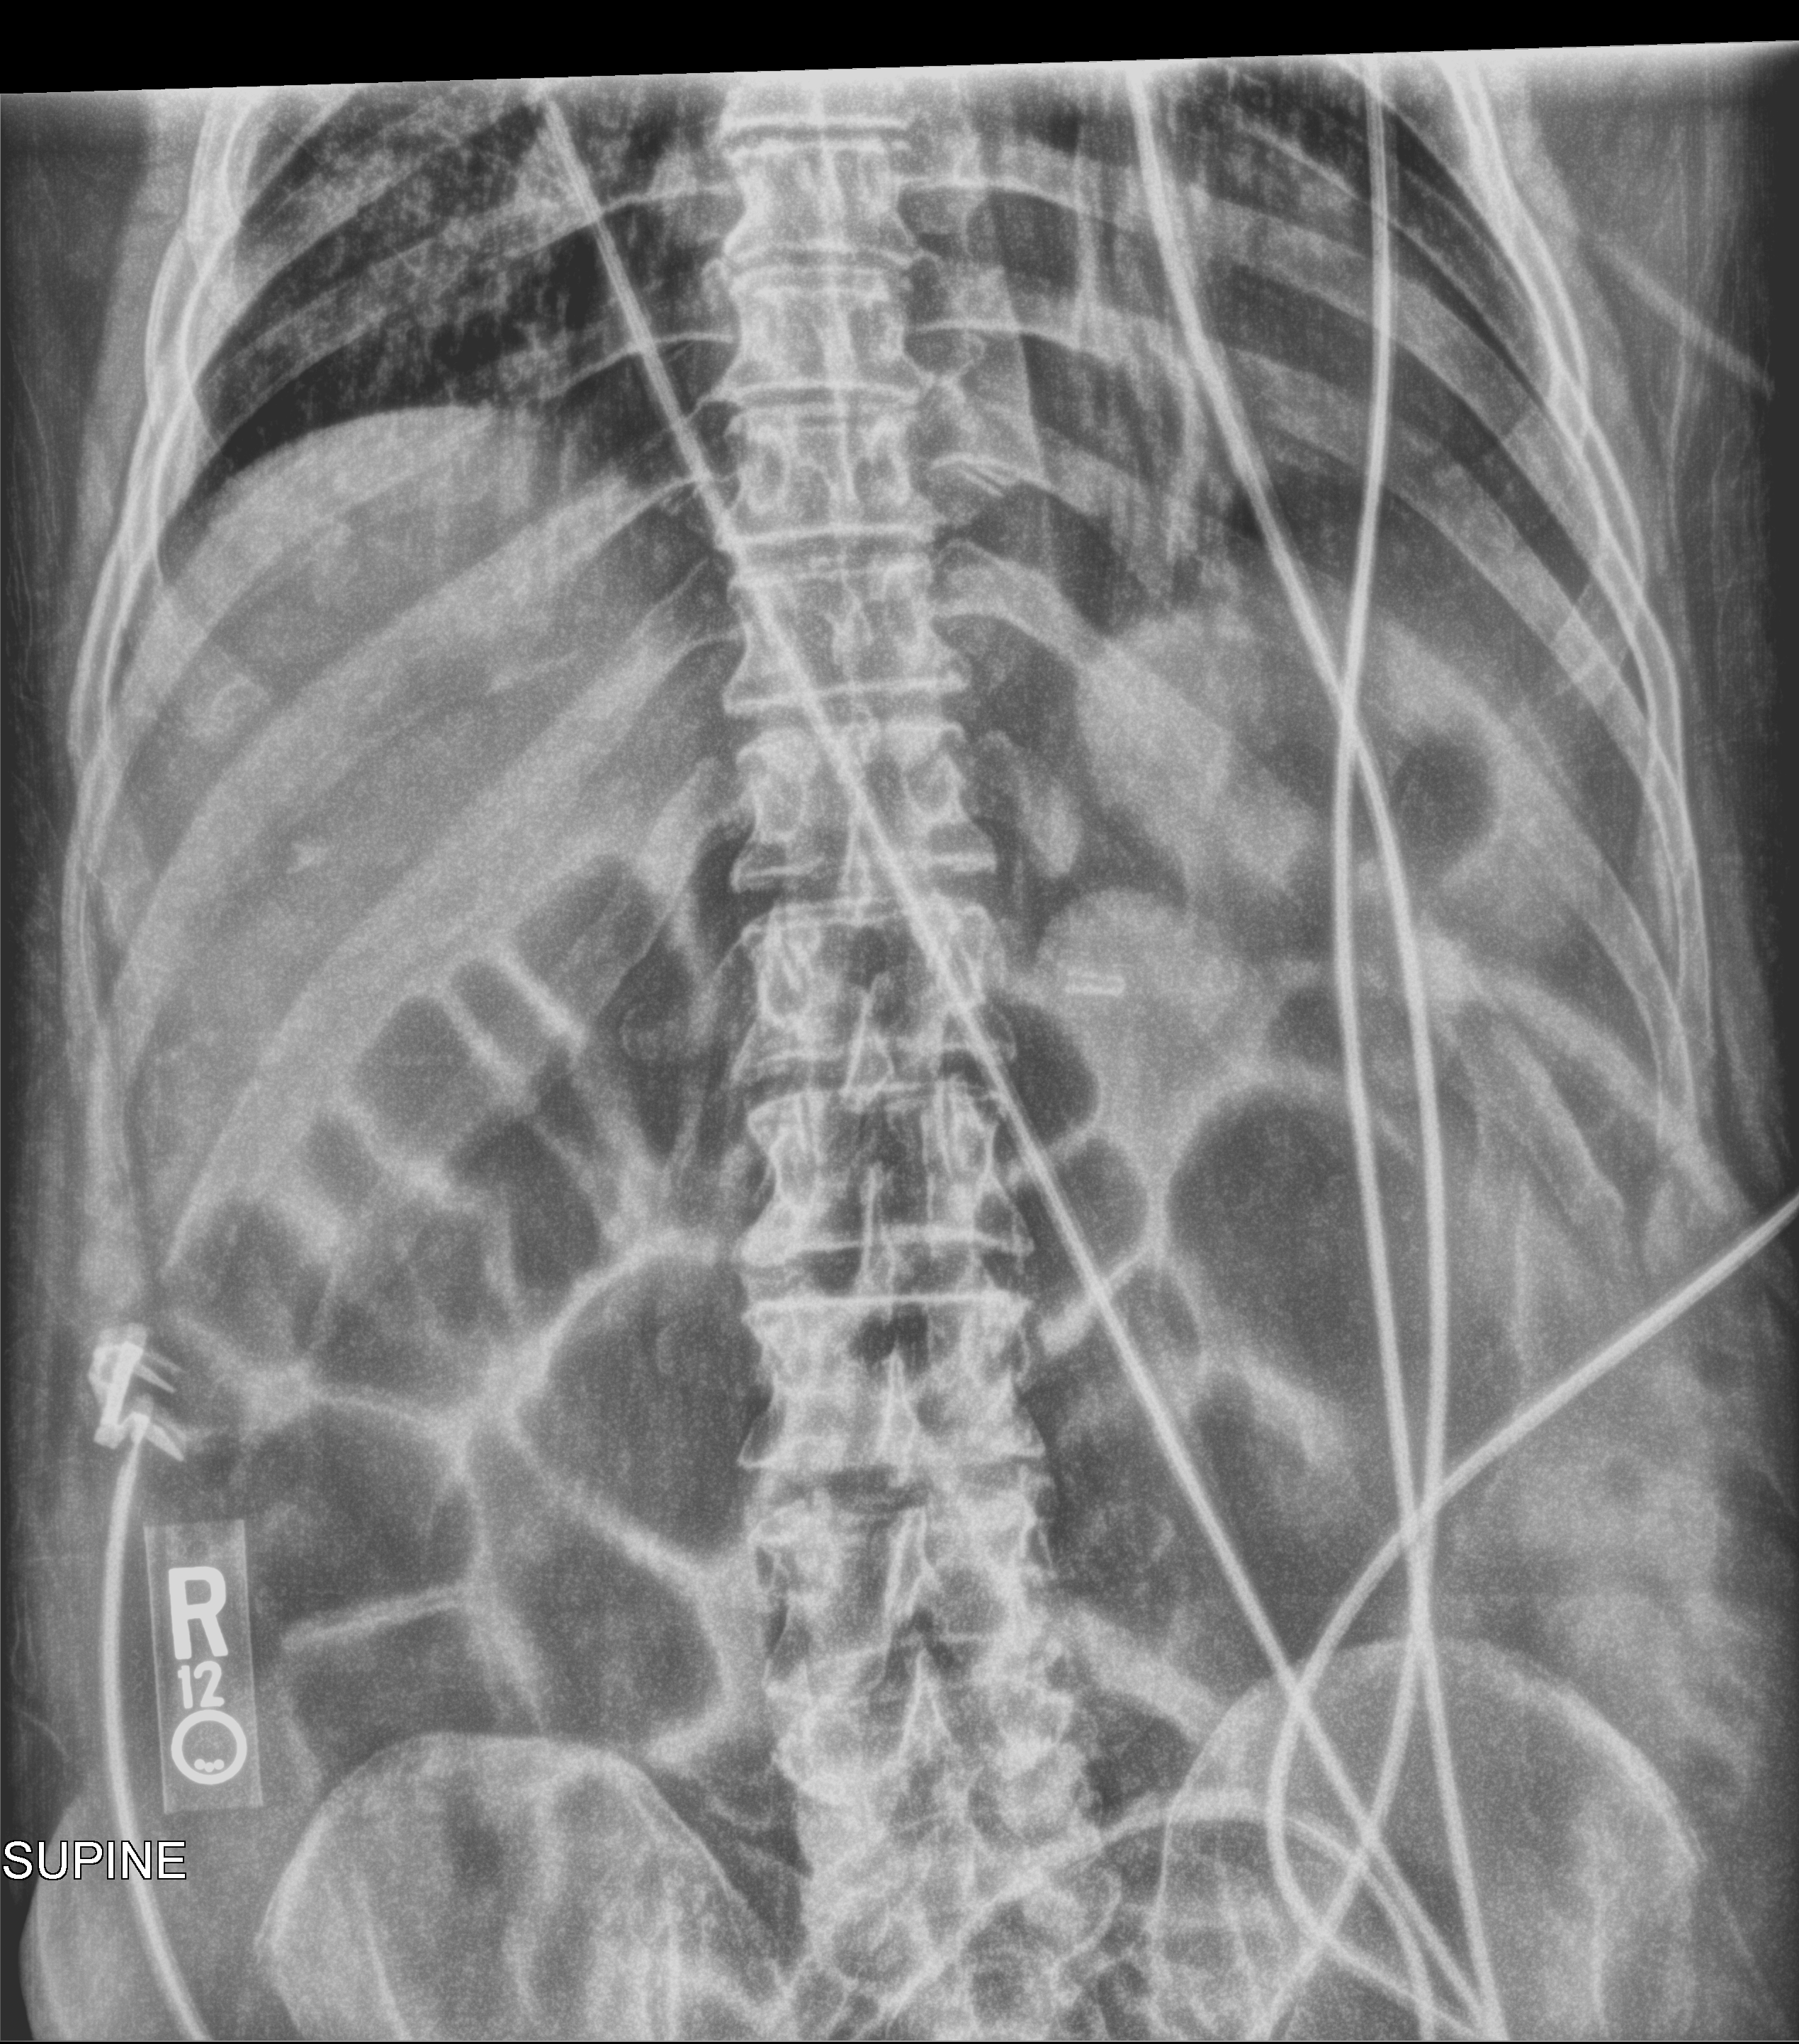
Portable abdomen radiograph, anteroposterior (AP) projection. Patient hospitalised with COVID-19; male, aged 60–74 years.
Admission-level facts for this patient (not findings on this image; timing relative to this image not recorded): mechanically ventilated during this hospital stay: no; admitted to intensive care during this hospital stay: no.